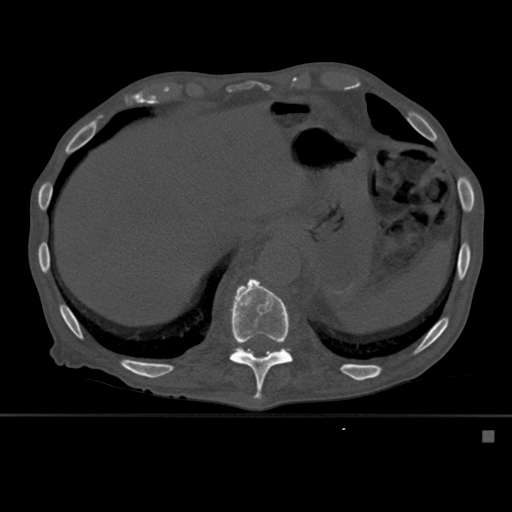
CT including the spine, one axial slice. Slice 294 of 527 in the series (ordered by position). Bone window (W 1800 / L 400 HU). 1.5 mm slice thickness. 512 × 512 image matrix, field of view 373 × 373 mm. Patient: male, 78 years. Case-level facts recorded for this patient, not image findings: primary cancer: prostate.
Structures marked on this image (semi-automatically segmented with operator editing):
- T11 vertebra: bounding box (x1, y1, x2, y2) in pixels: (229, 276, 294, 401)
- T12 vertebra: (277, 350, 281, 352)